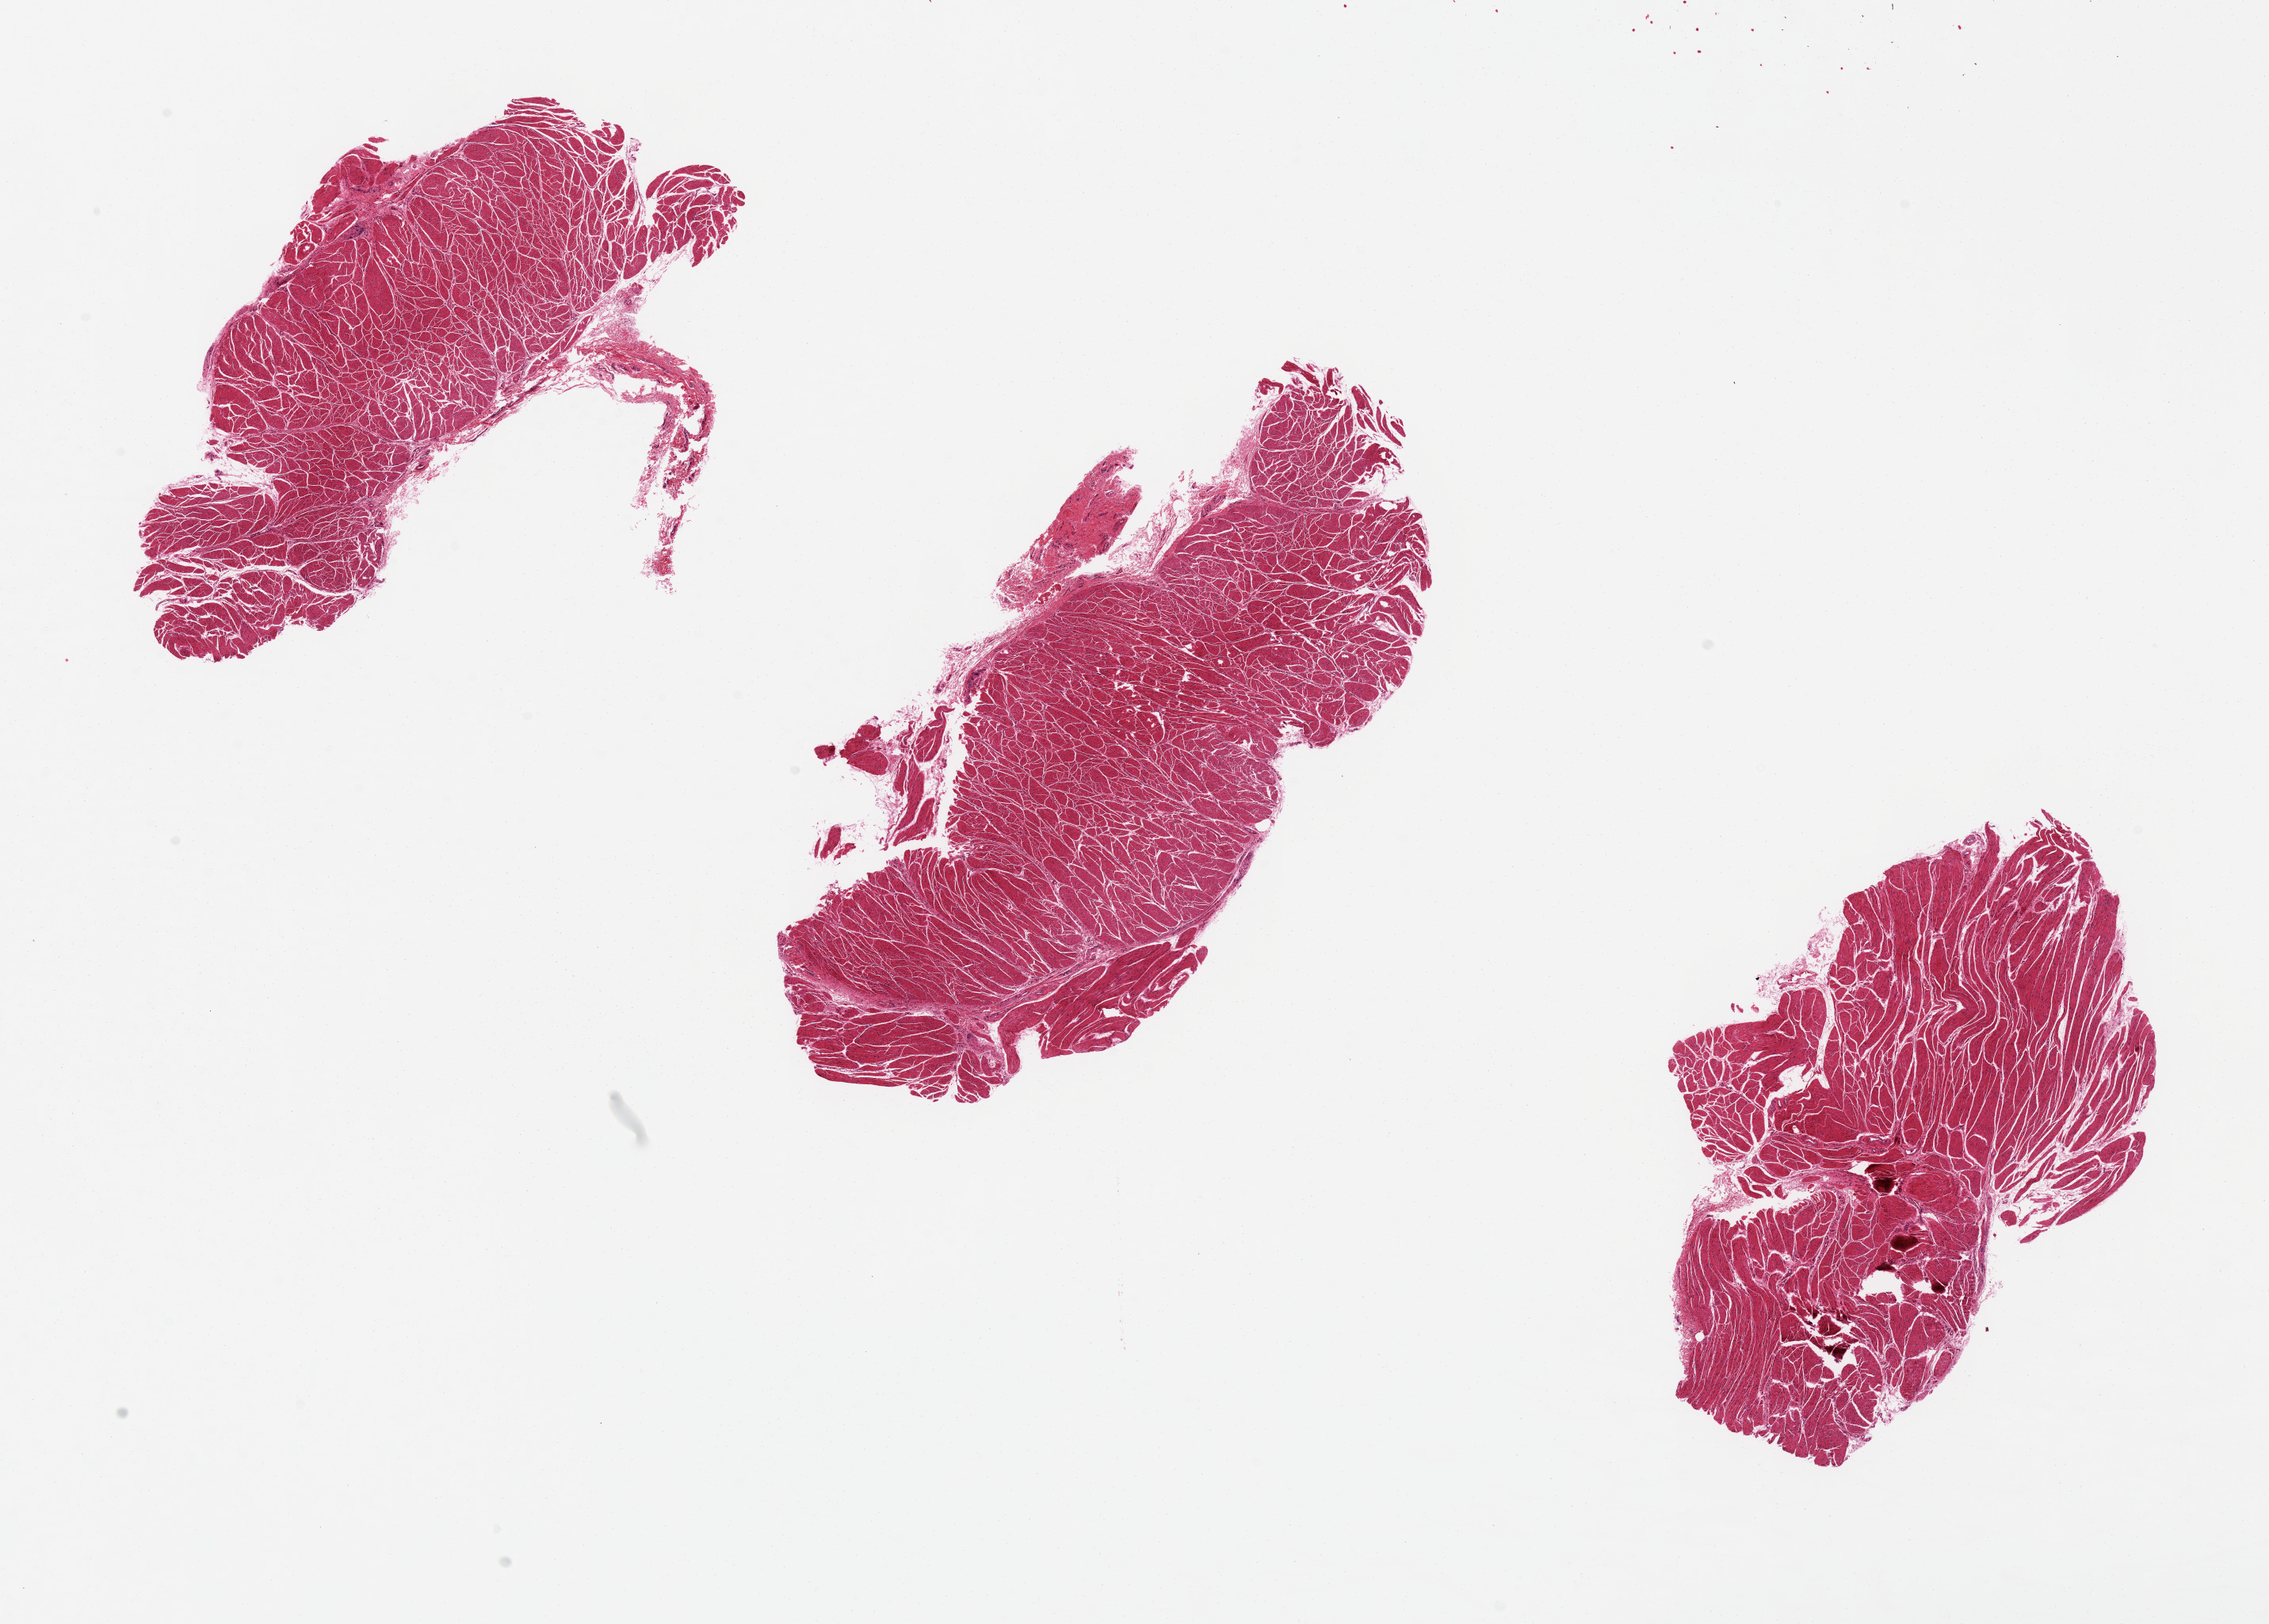
Haematoxylin and eosin whole-slide image, brightfield — low-resolution overview of the scanned area, about 22.6 x 16.2 mm (acquisition: 20x scan). PAXgene-fixed paraffin-embedded (PFPE) section. Target tissue: esophageal muscle. Donor tissue sample. Donor: male.
- reviewer comment on this tissue sample: Adequate for study